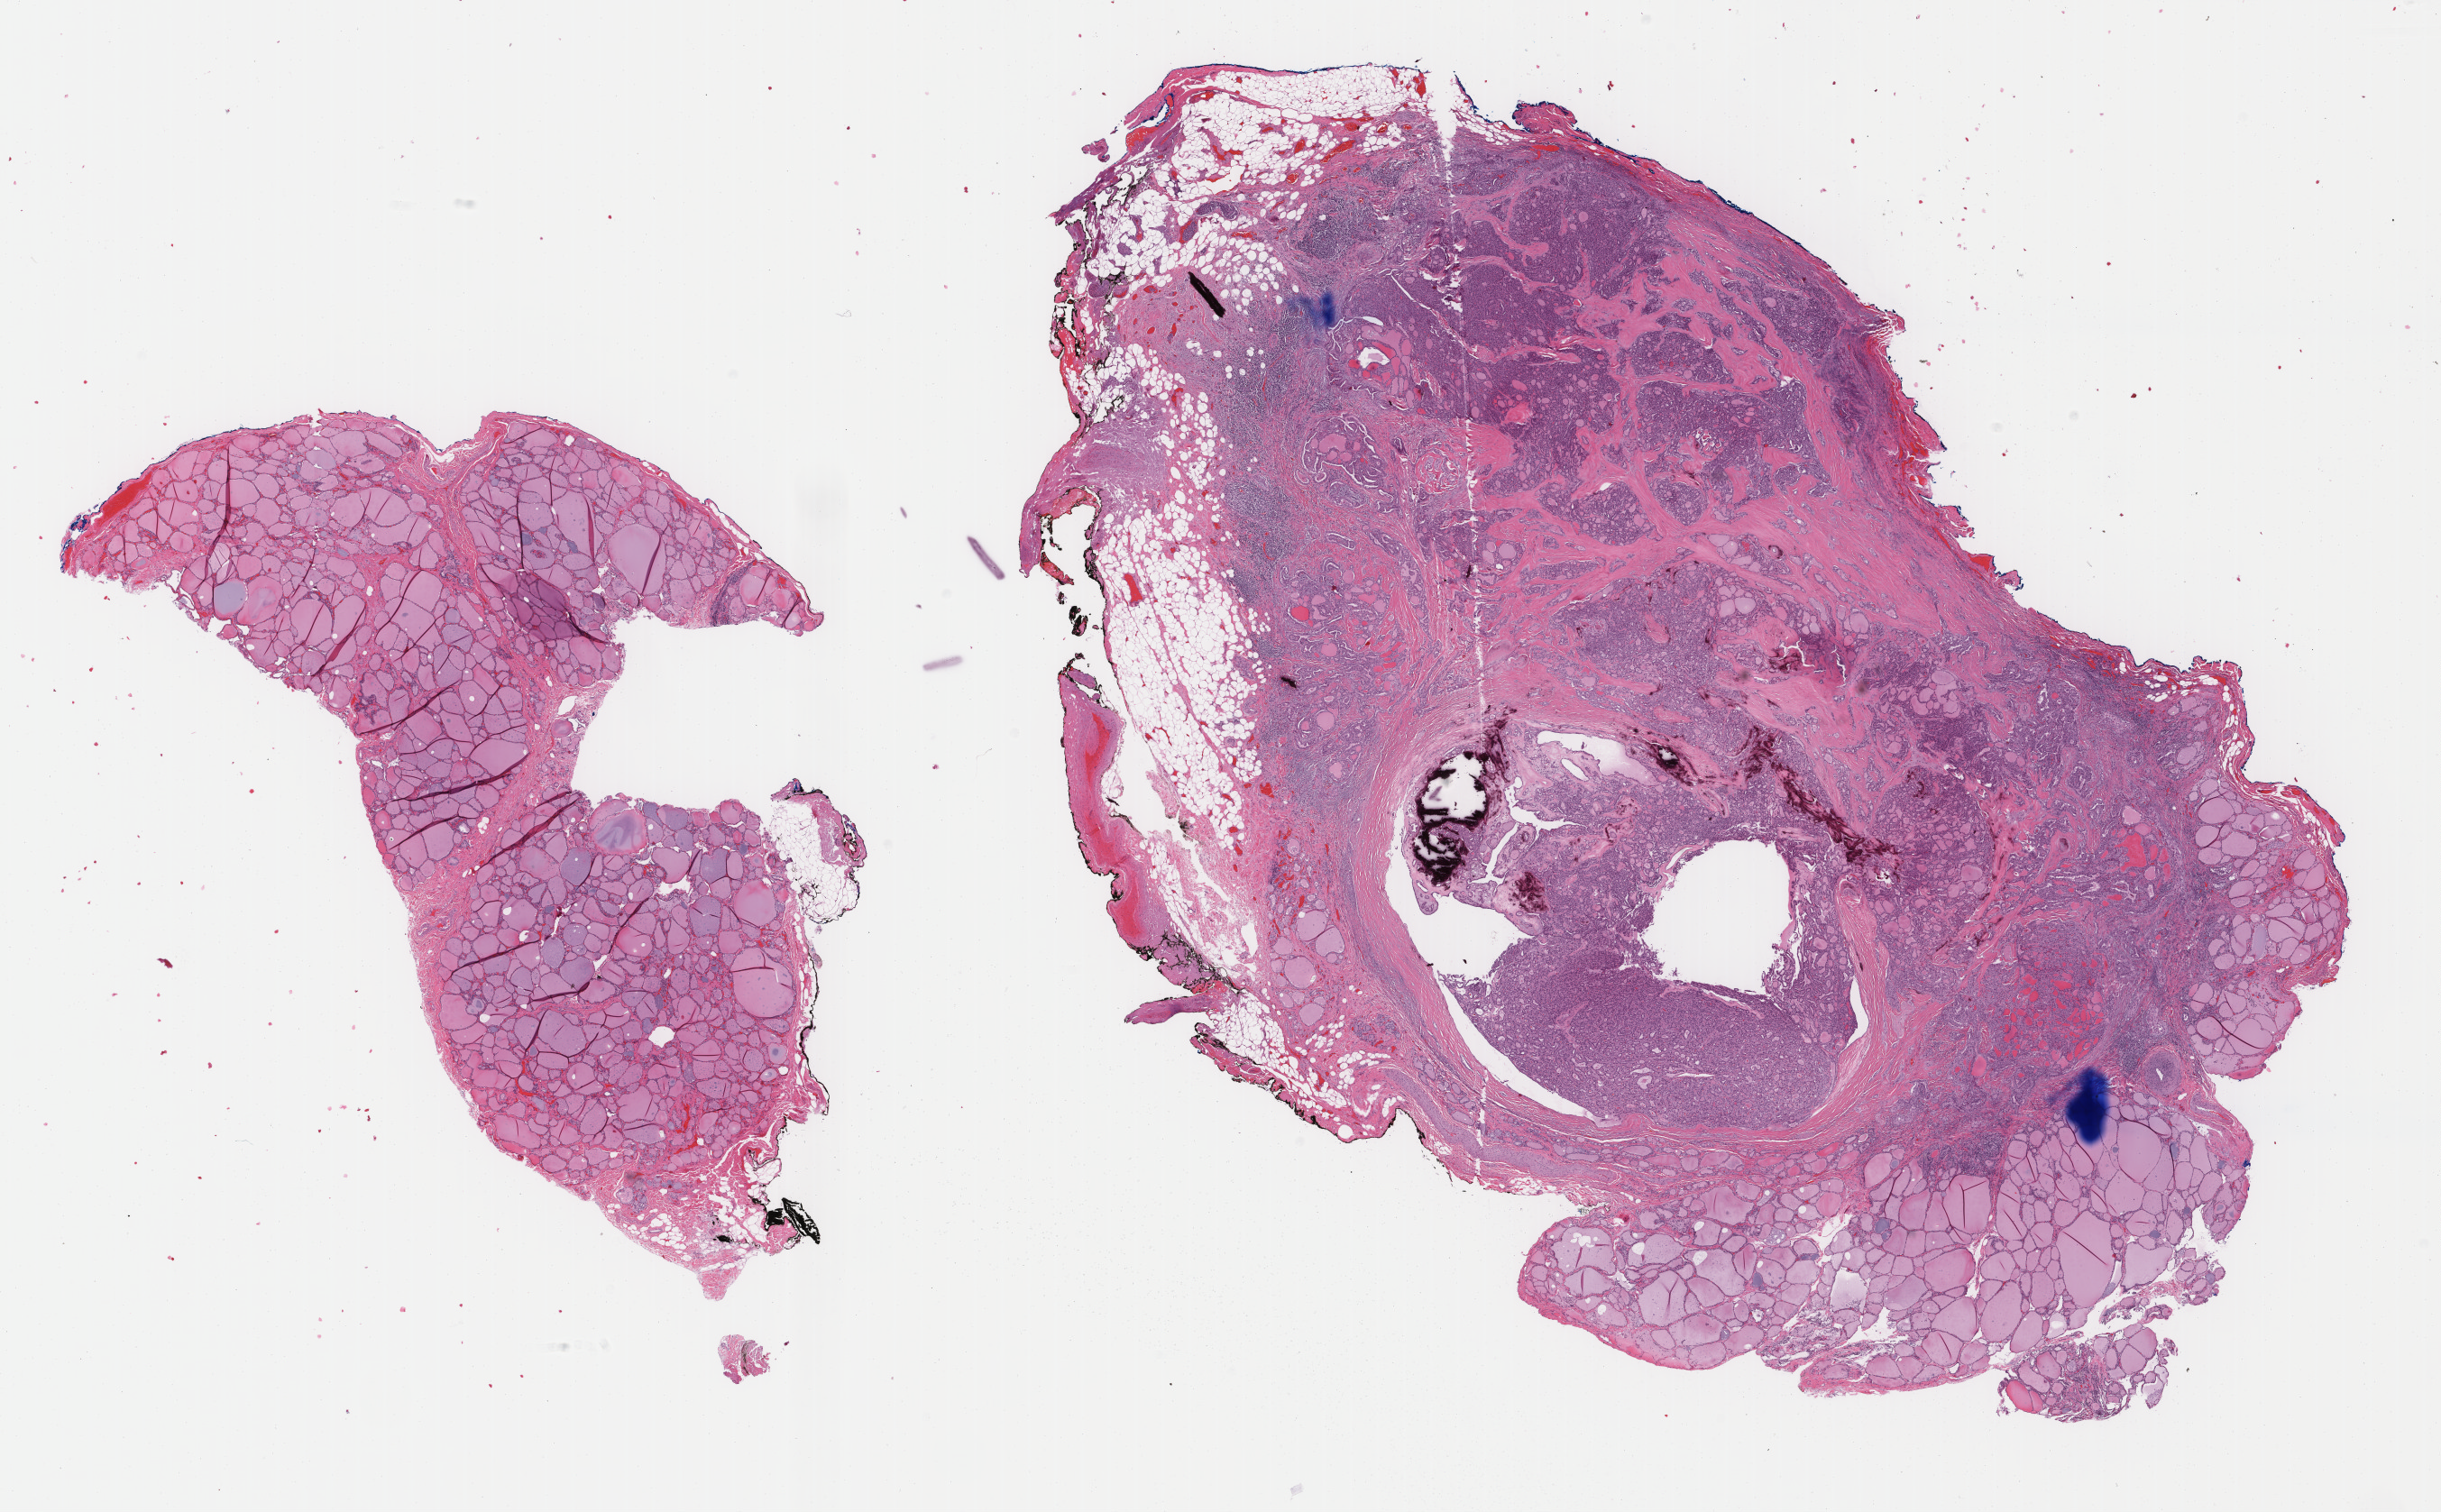
Hematoxylin and eosin (H&E) stained whole-slide image — whole scanned area (about 21.5 x 13.3 mm) shown as a low-resolution overview, formalin-fixed paraffin-embedded (FFPE) diagnostic section, thyroid, primary tumour sample. Patient: male, age at initial diagnosis 60 years.
• pathologic diagnosis: Papillary adenocarcinoma, NOS
• AJCC pathologic stage: III (7th edition)